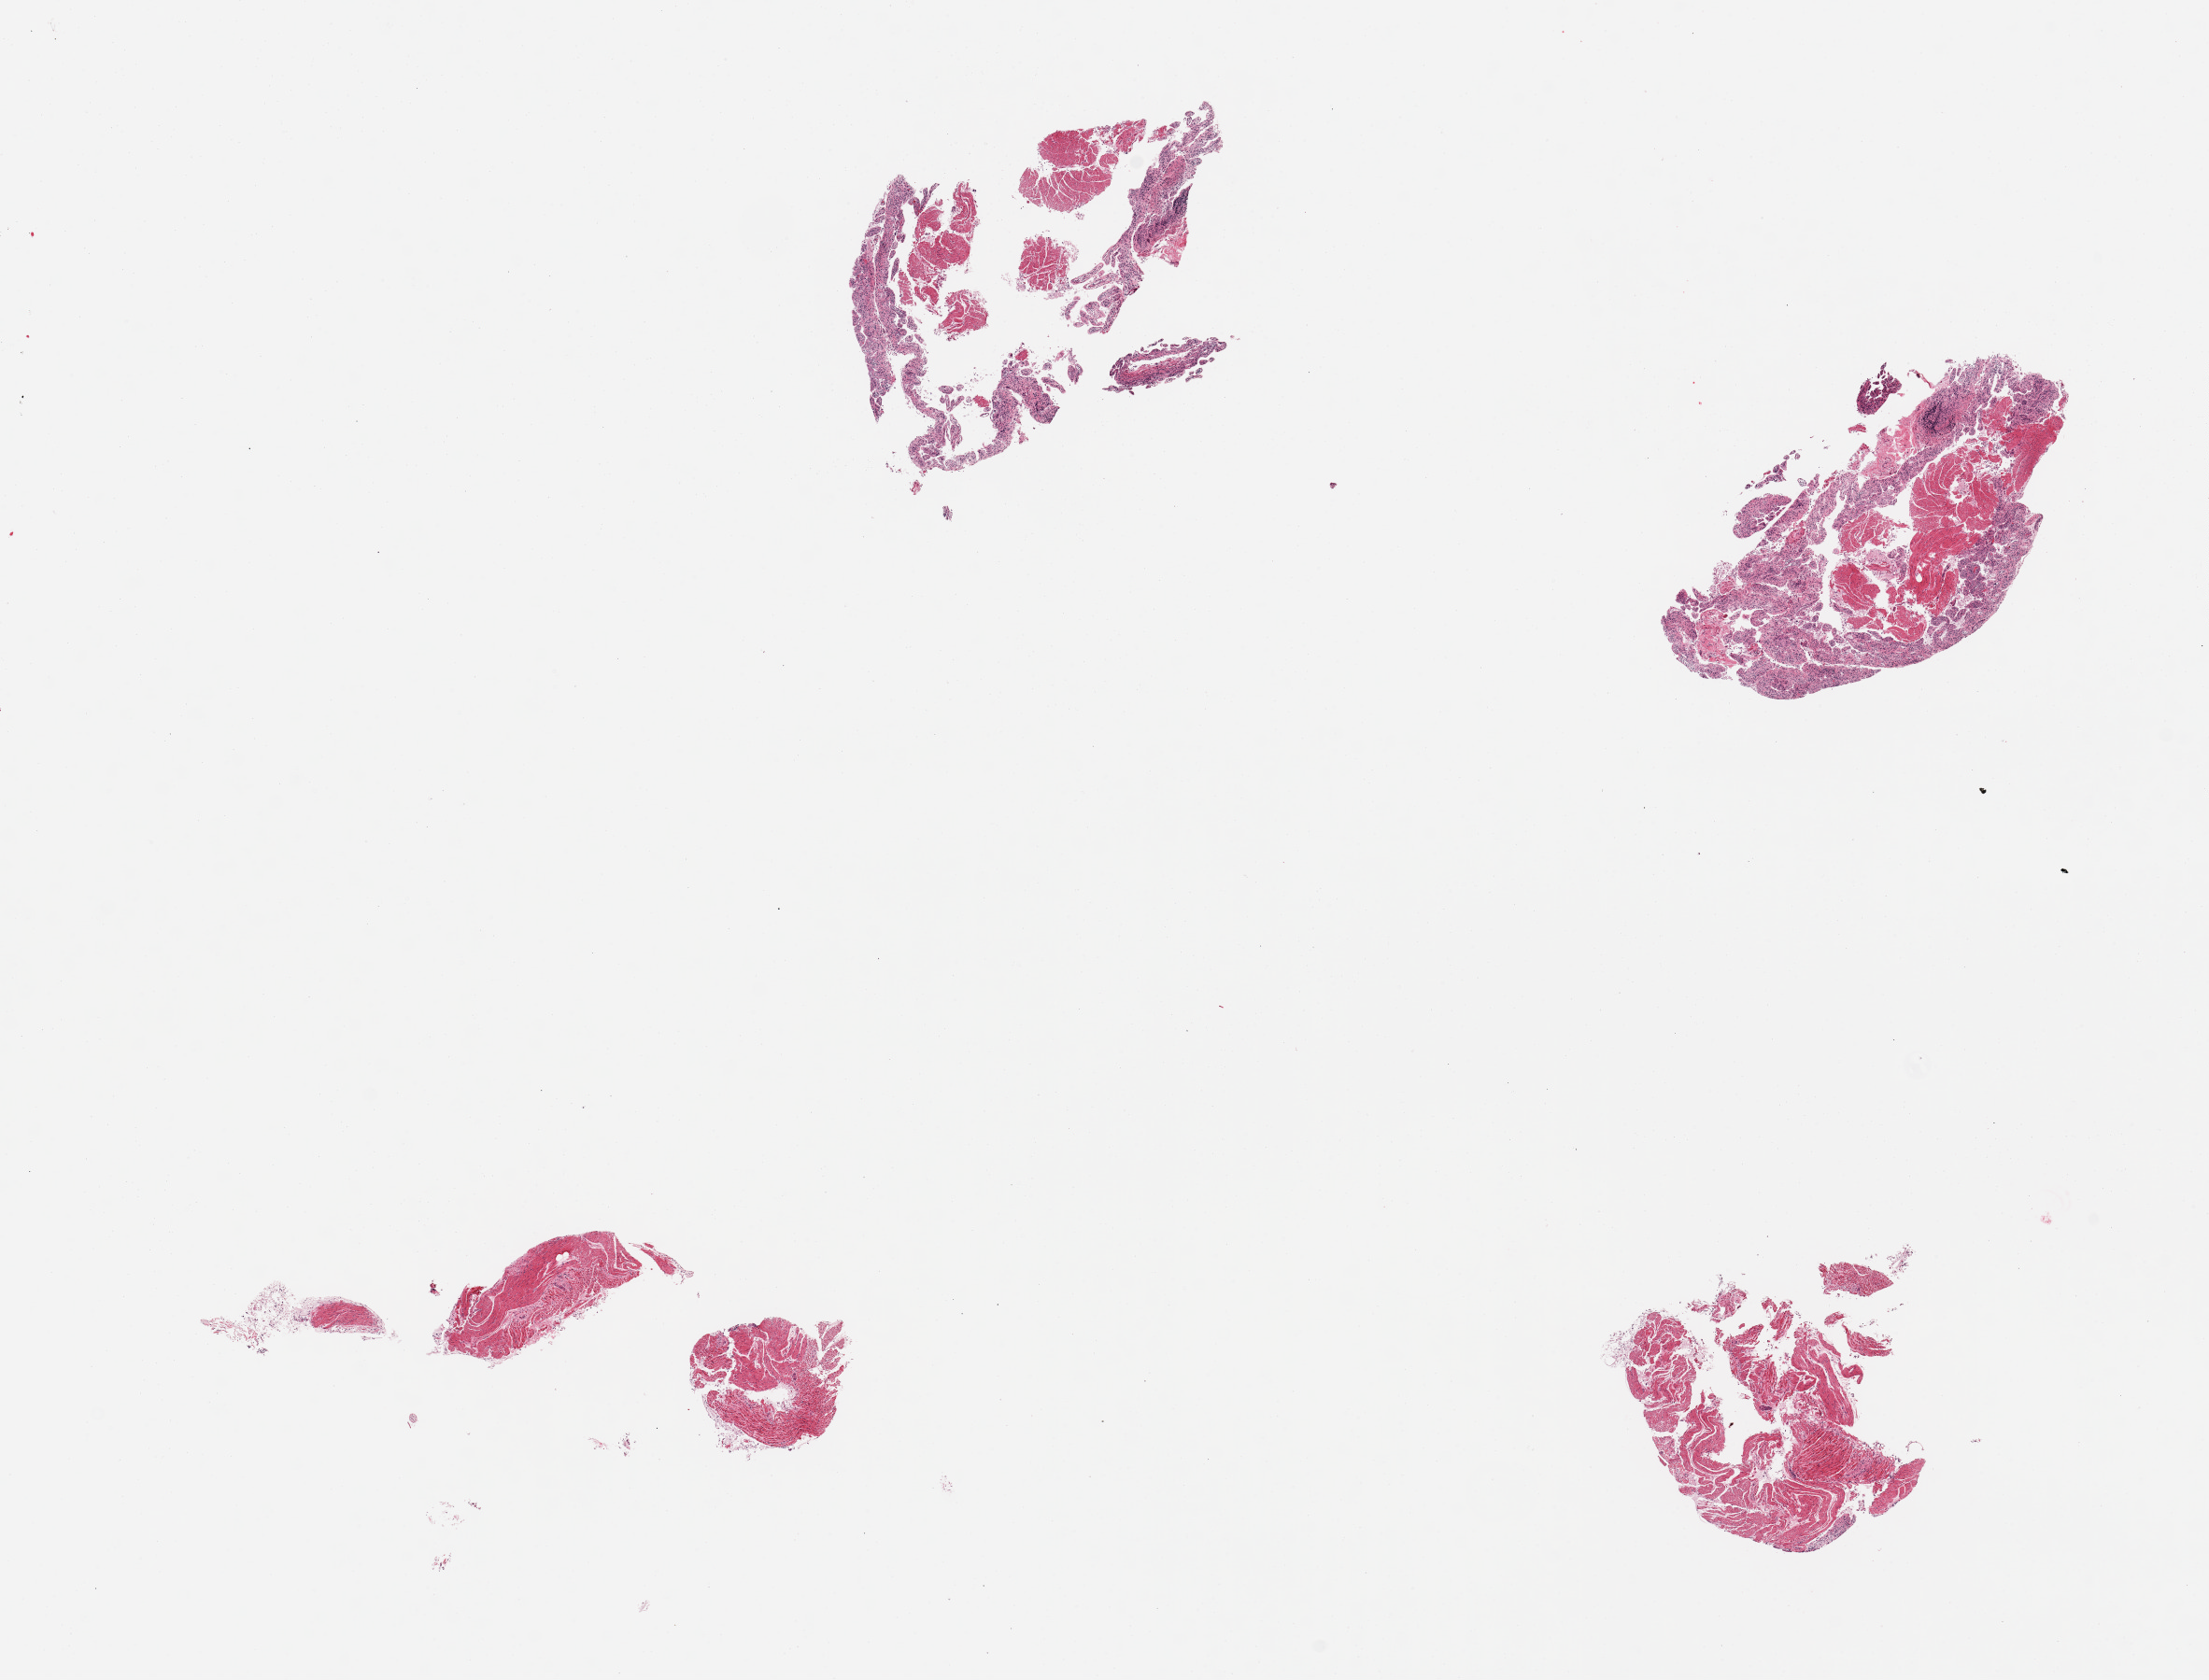
Digitized H&E-stained section, shown as a low-resolution overview of the whole scanned area (about 18.7 x 14.2 mm), PAXgene-fixed paraffin-embedded (PFPE) section, target tissue: ileum, tissue donor sample.
Reviewer comment on this tissue sample: 4 pieces; no lymphoid tissue.